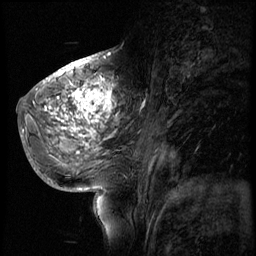
Breast MRI (dynamic contrast-enhanced), one sagittal slice; slice 28 of 56 in the series (ordered by position); 4 images stored at this slice position (order not interpretable as contrast timing); 1.5 T; TE 4.2 ms, TR 8.9 ms; 256 × 256 image matrix. Patient: female, 51 years. From the clinical record (not read from this slice): setting: breast cancer imaged before/during neoadjuvant chemotherapy; receptor status: triple-negative.
Annotated regions visible in this slice (semi-automatically segmented with operator editing):
- analysis volume of interest (the breast-tissue region the enhancement analysis was run in; not a lesion): bounding box [x1, y1, x2, y2] px = [30, 70, 150, 173]
- tumour enhancement mask (voxels above the 140 % enhancement threshold inside the analysis volume of interest): [46, 72, 115, 137]